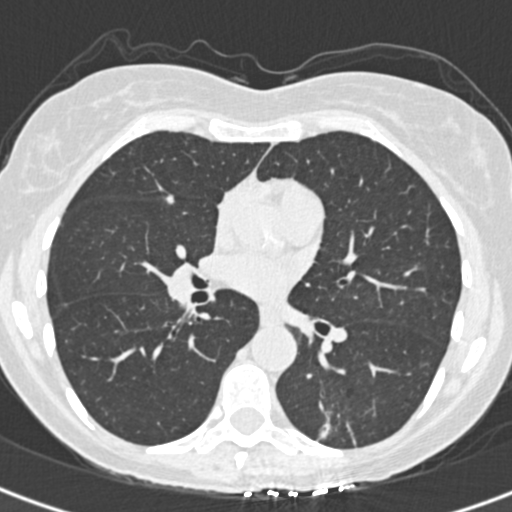
Low-dose screening chest CT, one axial slice. Slice 184 of 328 in the series (ordered by position). Reconstruction kernel B30f. 120 kVp. Lung window (W 1500 / L -600 HU). 1 mm slice thickness. 512 × 512 image matrix, field of view 284 × 284 mm.
Structures marked on this image (expert manual segmentation):
- lesion 1 (tumor, lower lobe of left lung): bounding box (x1, y1, x2, y2) in pixels: (322, 423, 329, 437)